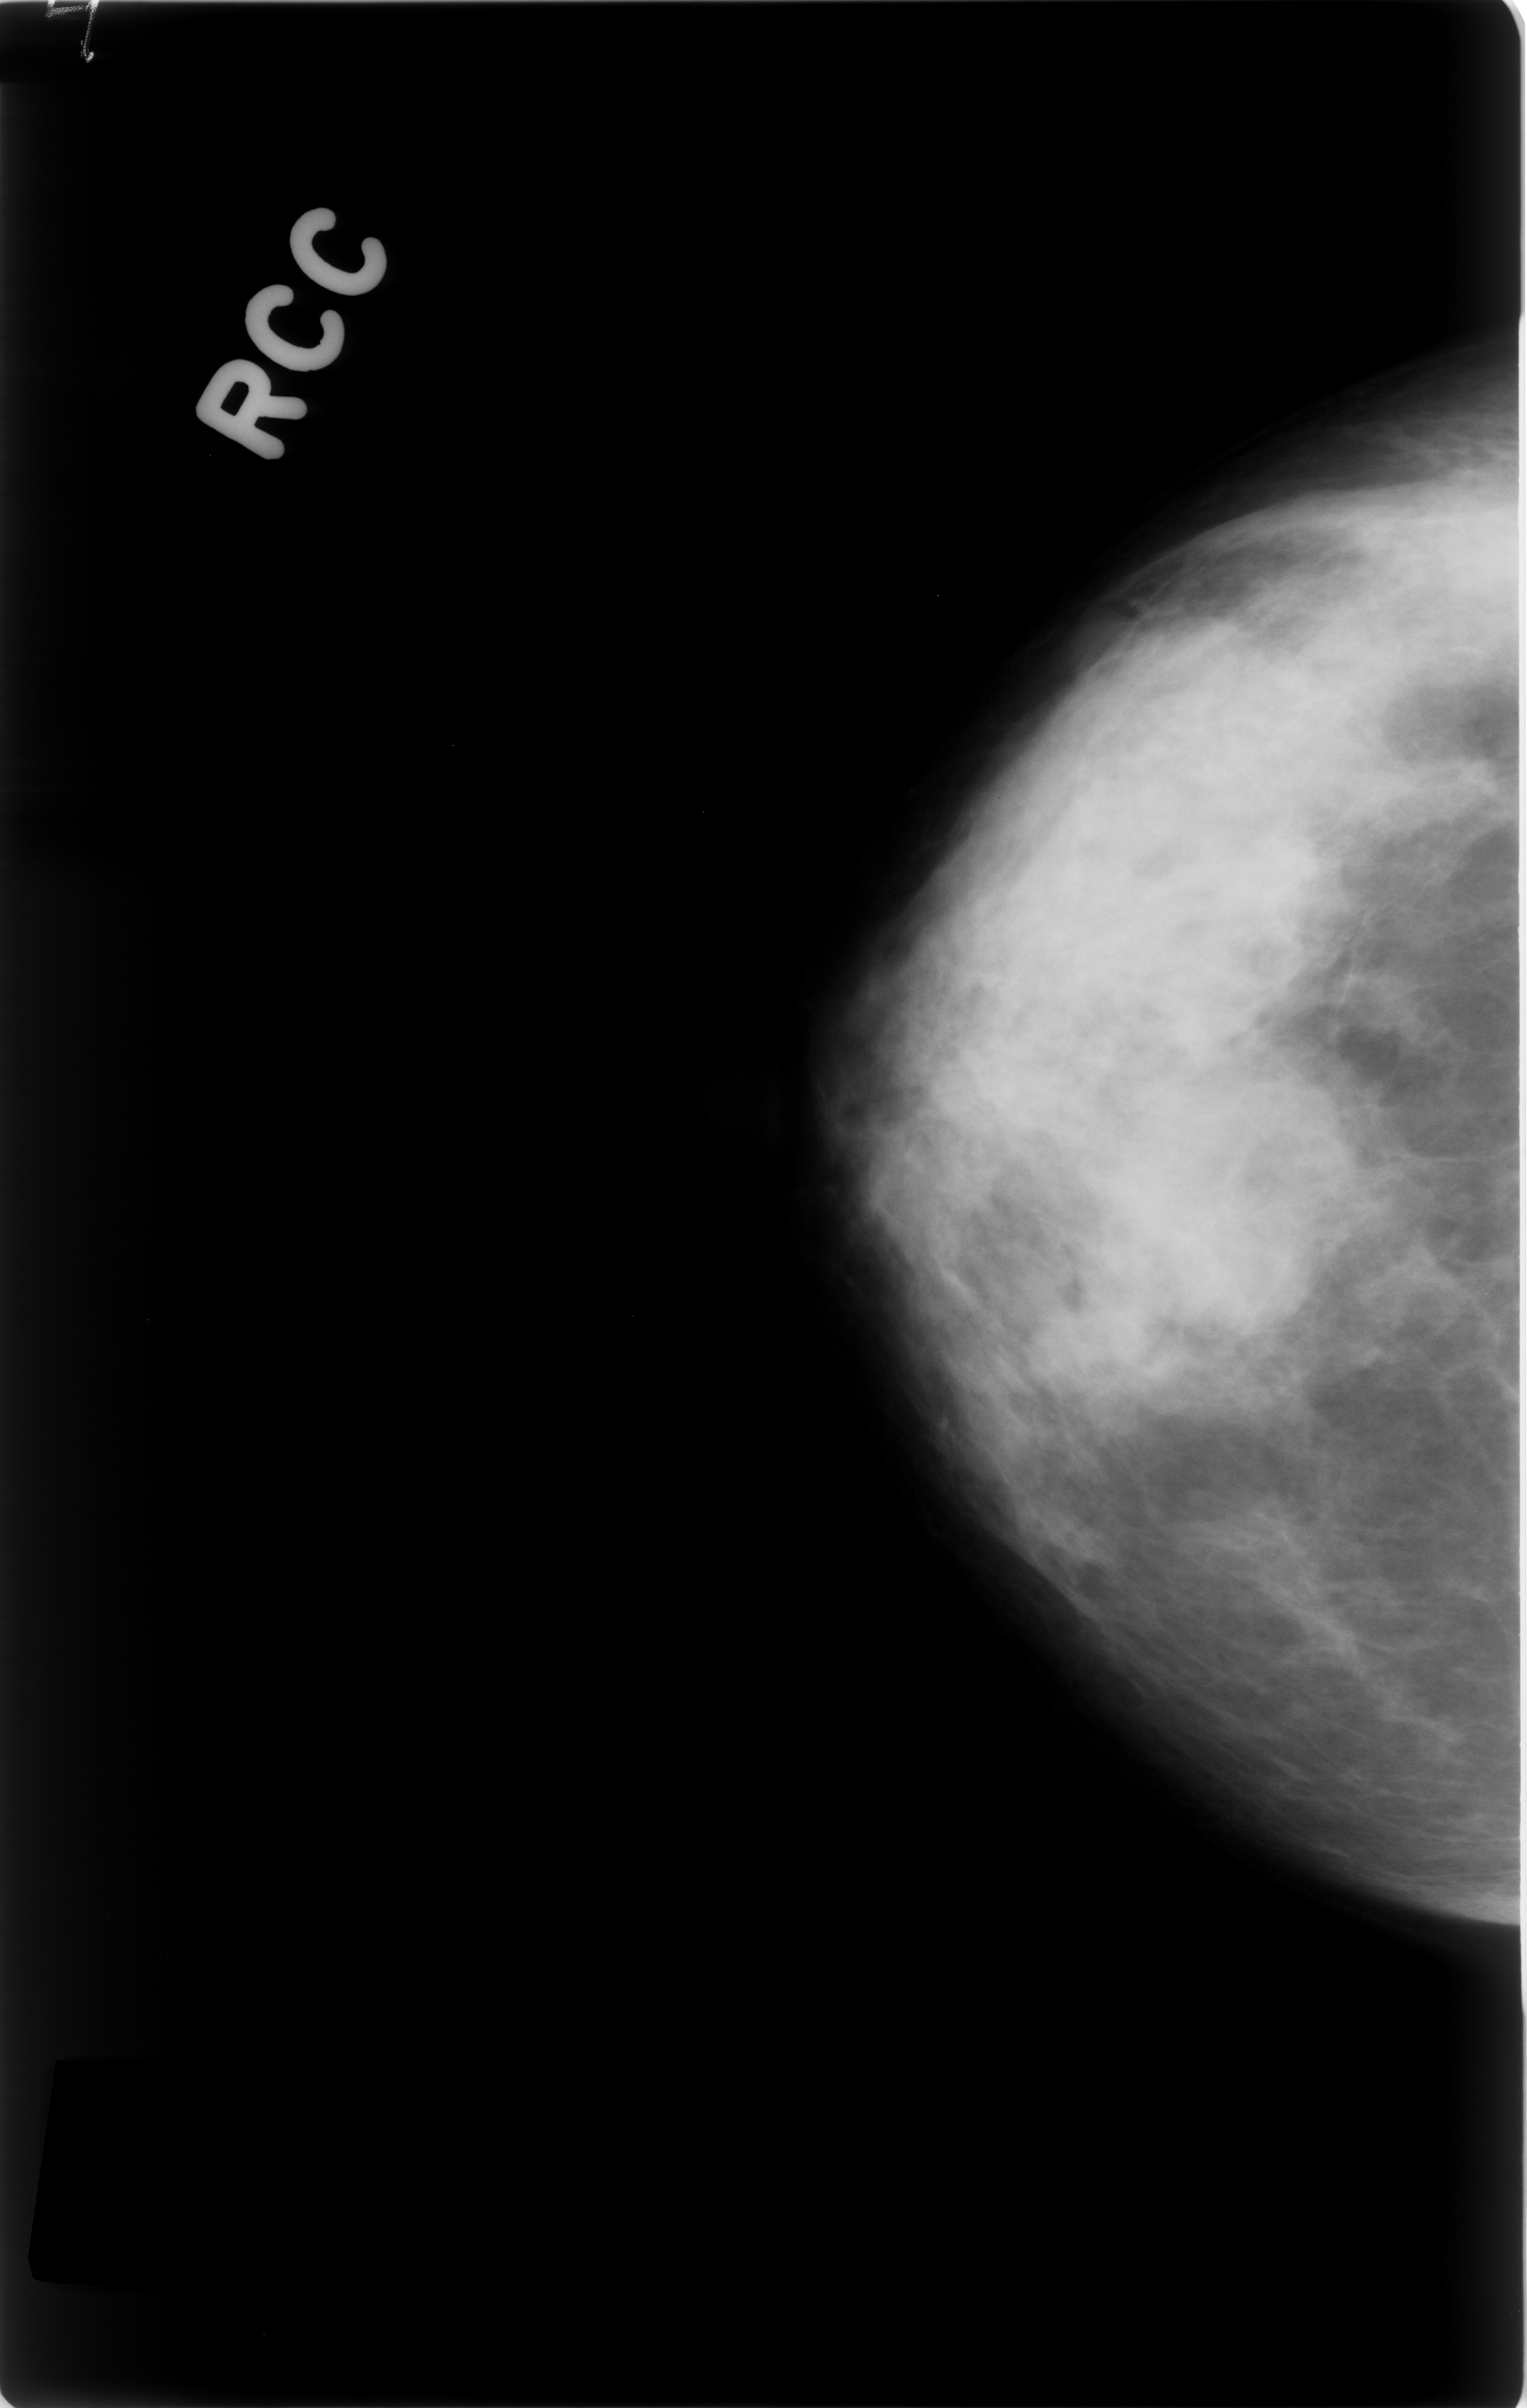
Mammogram (digitized film), right breast, CC view.
- Mass, shape lobulated, margins obscured; BI-RADS assessment category 3; subtlety rating 4 on a 1 (subtle) to 5 (obvious) scale; pathology result (as recorded, not read from the image): benign.